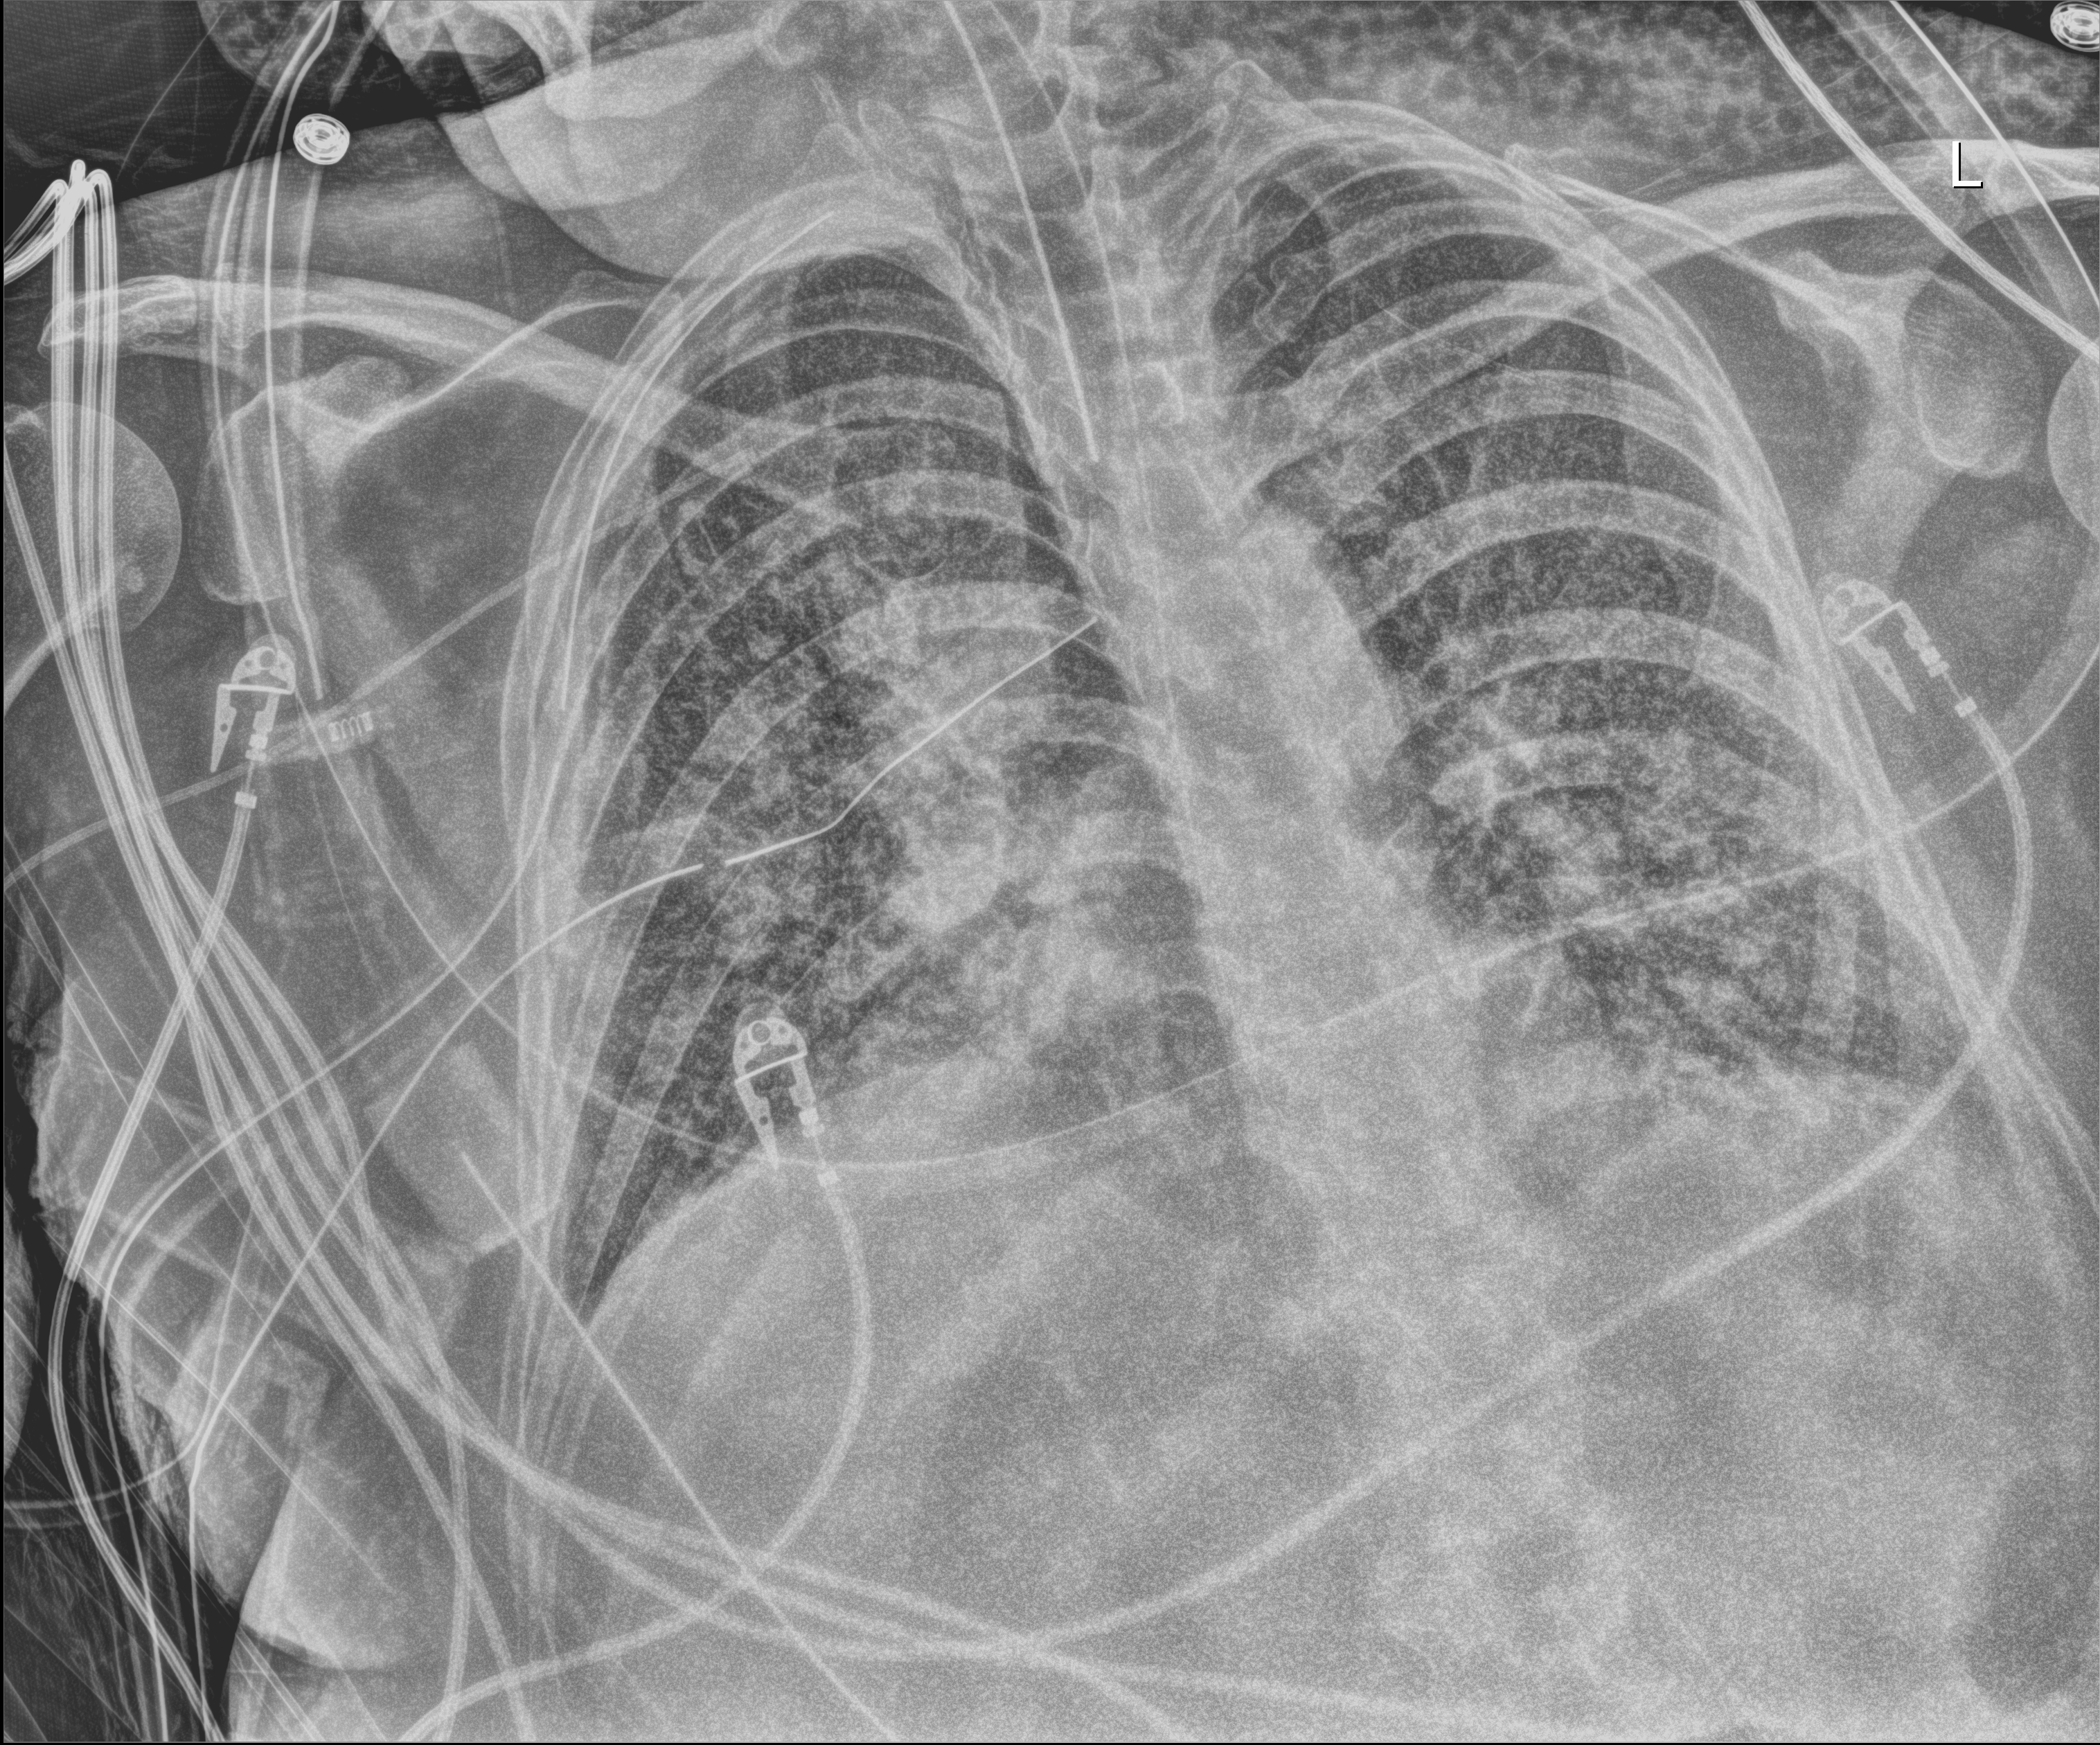
Chest X-ray (portable), anteroposterior (AP) projection. Patient hospitalised with COVID-19, aged 18–59 years.
Admission-level facts for this patient (not findings on this image; timing relative to this image not recorded): mechanically ventilated during this hospital stay: yes; diabetes (admission record): no; admitted to intensive care during this hospital stay: yes.